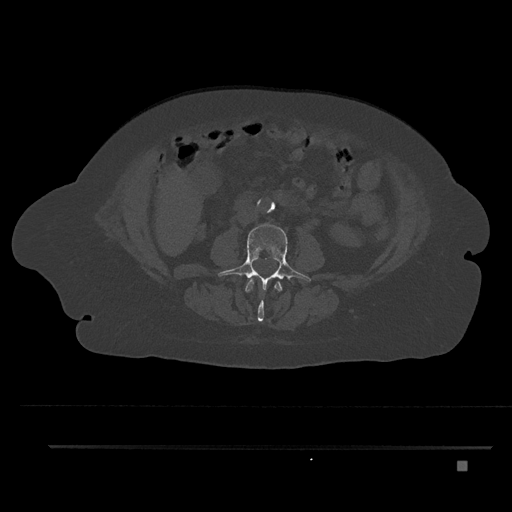
CT including the spine, one axial slice; slice 133 of 797 in the series (ordered by position); 120 kVp; bone window (W 1800 / L 400 HU); 0.5 mm slice thickness; 512 × 512 image matrix, field of view 437 × 437 mm. Female patient, age 76 years. Case-level facts recorded for this patient, not image findings: primary cancer: lung; vertebrae with lytic lesions (as recorded): T11, L3.
Annotated regions visible in this slice (semi-automatic segmentation, software-assisted and operator-edited):
- L2 vertebra: bounding box (x1, y1, x2, y2) in pixels: (245, 279, 283, 322)
- L3 vertebra: (216, 223, 311, 291)